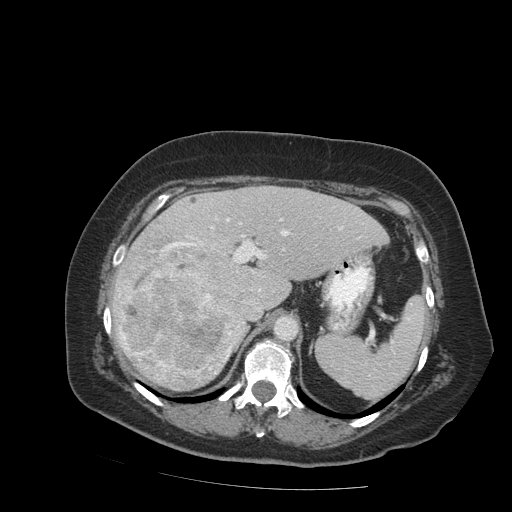
Contrast-enhanced abdominal CT (liver protocol), one axial slice. Slice 56 of 99 in the series (ordered by position). 140 kVp. Soft-tissue window (W 400 / L 40 HU). 2.5 mm slice thickness. 512 × 512 image matrix, field of view 400 × 400 mm. Case-level facts recorded for this patient, not image findings: diagnosis: hepatocellular carcinoma (patient treated with transarterial chemoembolisation; whether this scan precedes or follows treatment is not stated here); TNM stage (as recorded): Stage-IVB; Child-Pugh class: A; tumour differentiation: moderately differentiated.
Structures marked on this image (semi-automatically segmented with operator editing):
- liver parenchyma outside the tumour (the mass and vessels are separate outlines, so this box may not span the whole liver): box from (x=112, y=186) to (x=388, y=390) px
- mass: (x=114, y=226)–(x=240, y=388)
- liver vessels: (x=116, y=218)–(x=360, y=291)